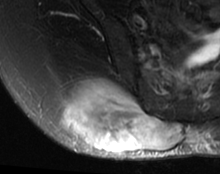
MRI of an extremity soft-tissue mass, one axial slice; position 36 of 63 along the scan axis; T2-weighted fat-saturated; MR volume resampled by the dataset authors to the PET/CT grid (not the native acquisition matrix); 3.27 mm slice thickness; 220 × 174 image matrix, field of view 215 × 170 mm. Female patient. From the clinical record (not read from this slice): histological type: spindle cell suggestive of myxofibrosarcoma; grade: intermediate; site of the primary tumour: right buttock.
Outlined on this slice (expert contour drawn on MRI and transferred to this co-registered scan by the dataset authors):
- gross tumour volume (mass): box from (x=63, y=82) to (x=183, y=153) px